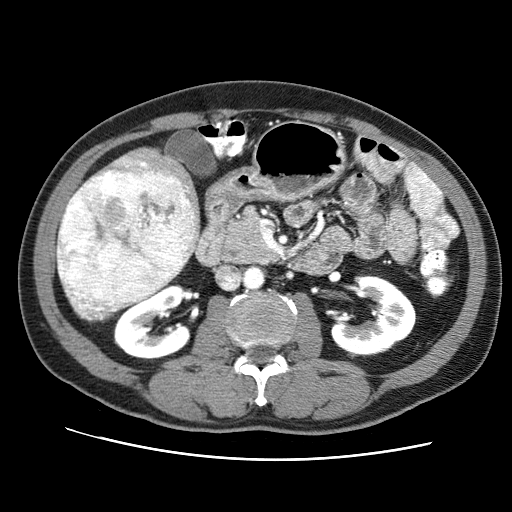
Contrast-enhanced abdominal CT (liver protocol), one axial slice. Slice 27 of 71 in the series (ordered by position). 120 kVp. Soft-tissue window (W 400 / L 40 HU). 2.5 mm slice thickness. 512 × 512 image matrix, field of view 360 × 360 mm. Case-level facts recorded for this patient, not image findings: diagnosis: hepatocellular carcinoma (patient treated with transarterial chemoembolisation; whether this scan precedes or follows treatment is not stated here); TNM stage (as recorded): Stage-II; Child-Pugh class: A; tumour differentiation: well differentiated; tumour nodularity: multinodular.
Annotated regions visible in this slice (semi-automatic segmentation, software-assisted and operator-edited):
- liver parenchyma outside the tumour (the mass and vessels are separate outlines, so this box may not span the whole liver): bounding box [x1, y1, x2, y2] px = [60, 146, 200, 307]
- mass: [56, 171, 200, 319]
- liver vessels: [117, 158, 188, 192]